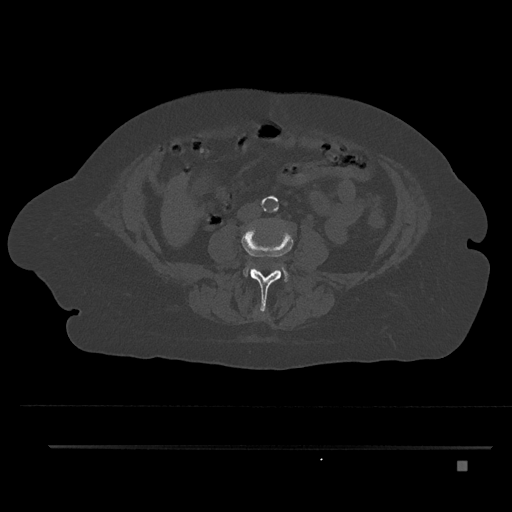
CT including the spine, one axial slice. Position 116 of 797 along the scan axis. Reconstruction kernel Br40s/3. 120 kVp. Bone window (W 1800 / L 400 HU). 0.5 mm slice thickness. 512 × 512 image matrix. Patient: female, 76 years. From the clinical record (not read from this slice): primary cancer: lung; vertebrae with lytic lesions (as recorded): T11, L3.
Structures marked on this image (semi-automatic segmentation, software-assisted and operator-edited):
- L2 vertebra: bounding box [x1, y1, x2, y2] px = [255, 309, 263, 315]
- L3 vertebra: [242, 226, 293, 311]
- L4 vertebra: [244, 263, 289, 282]